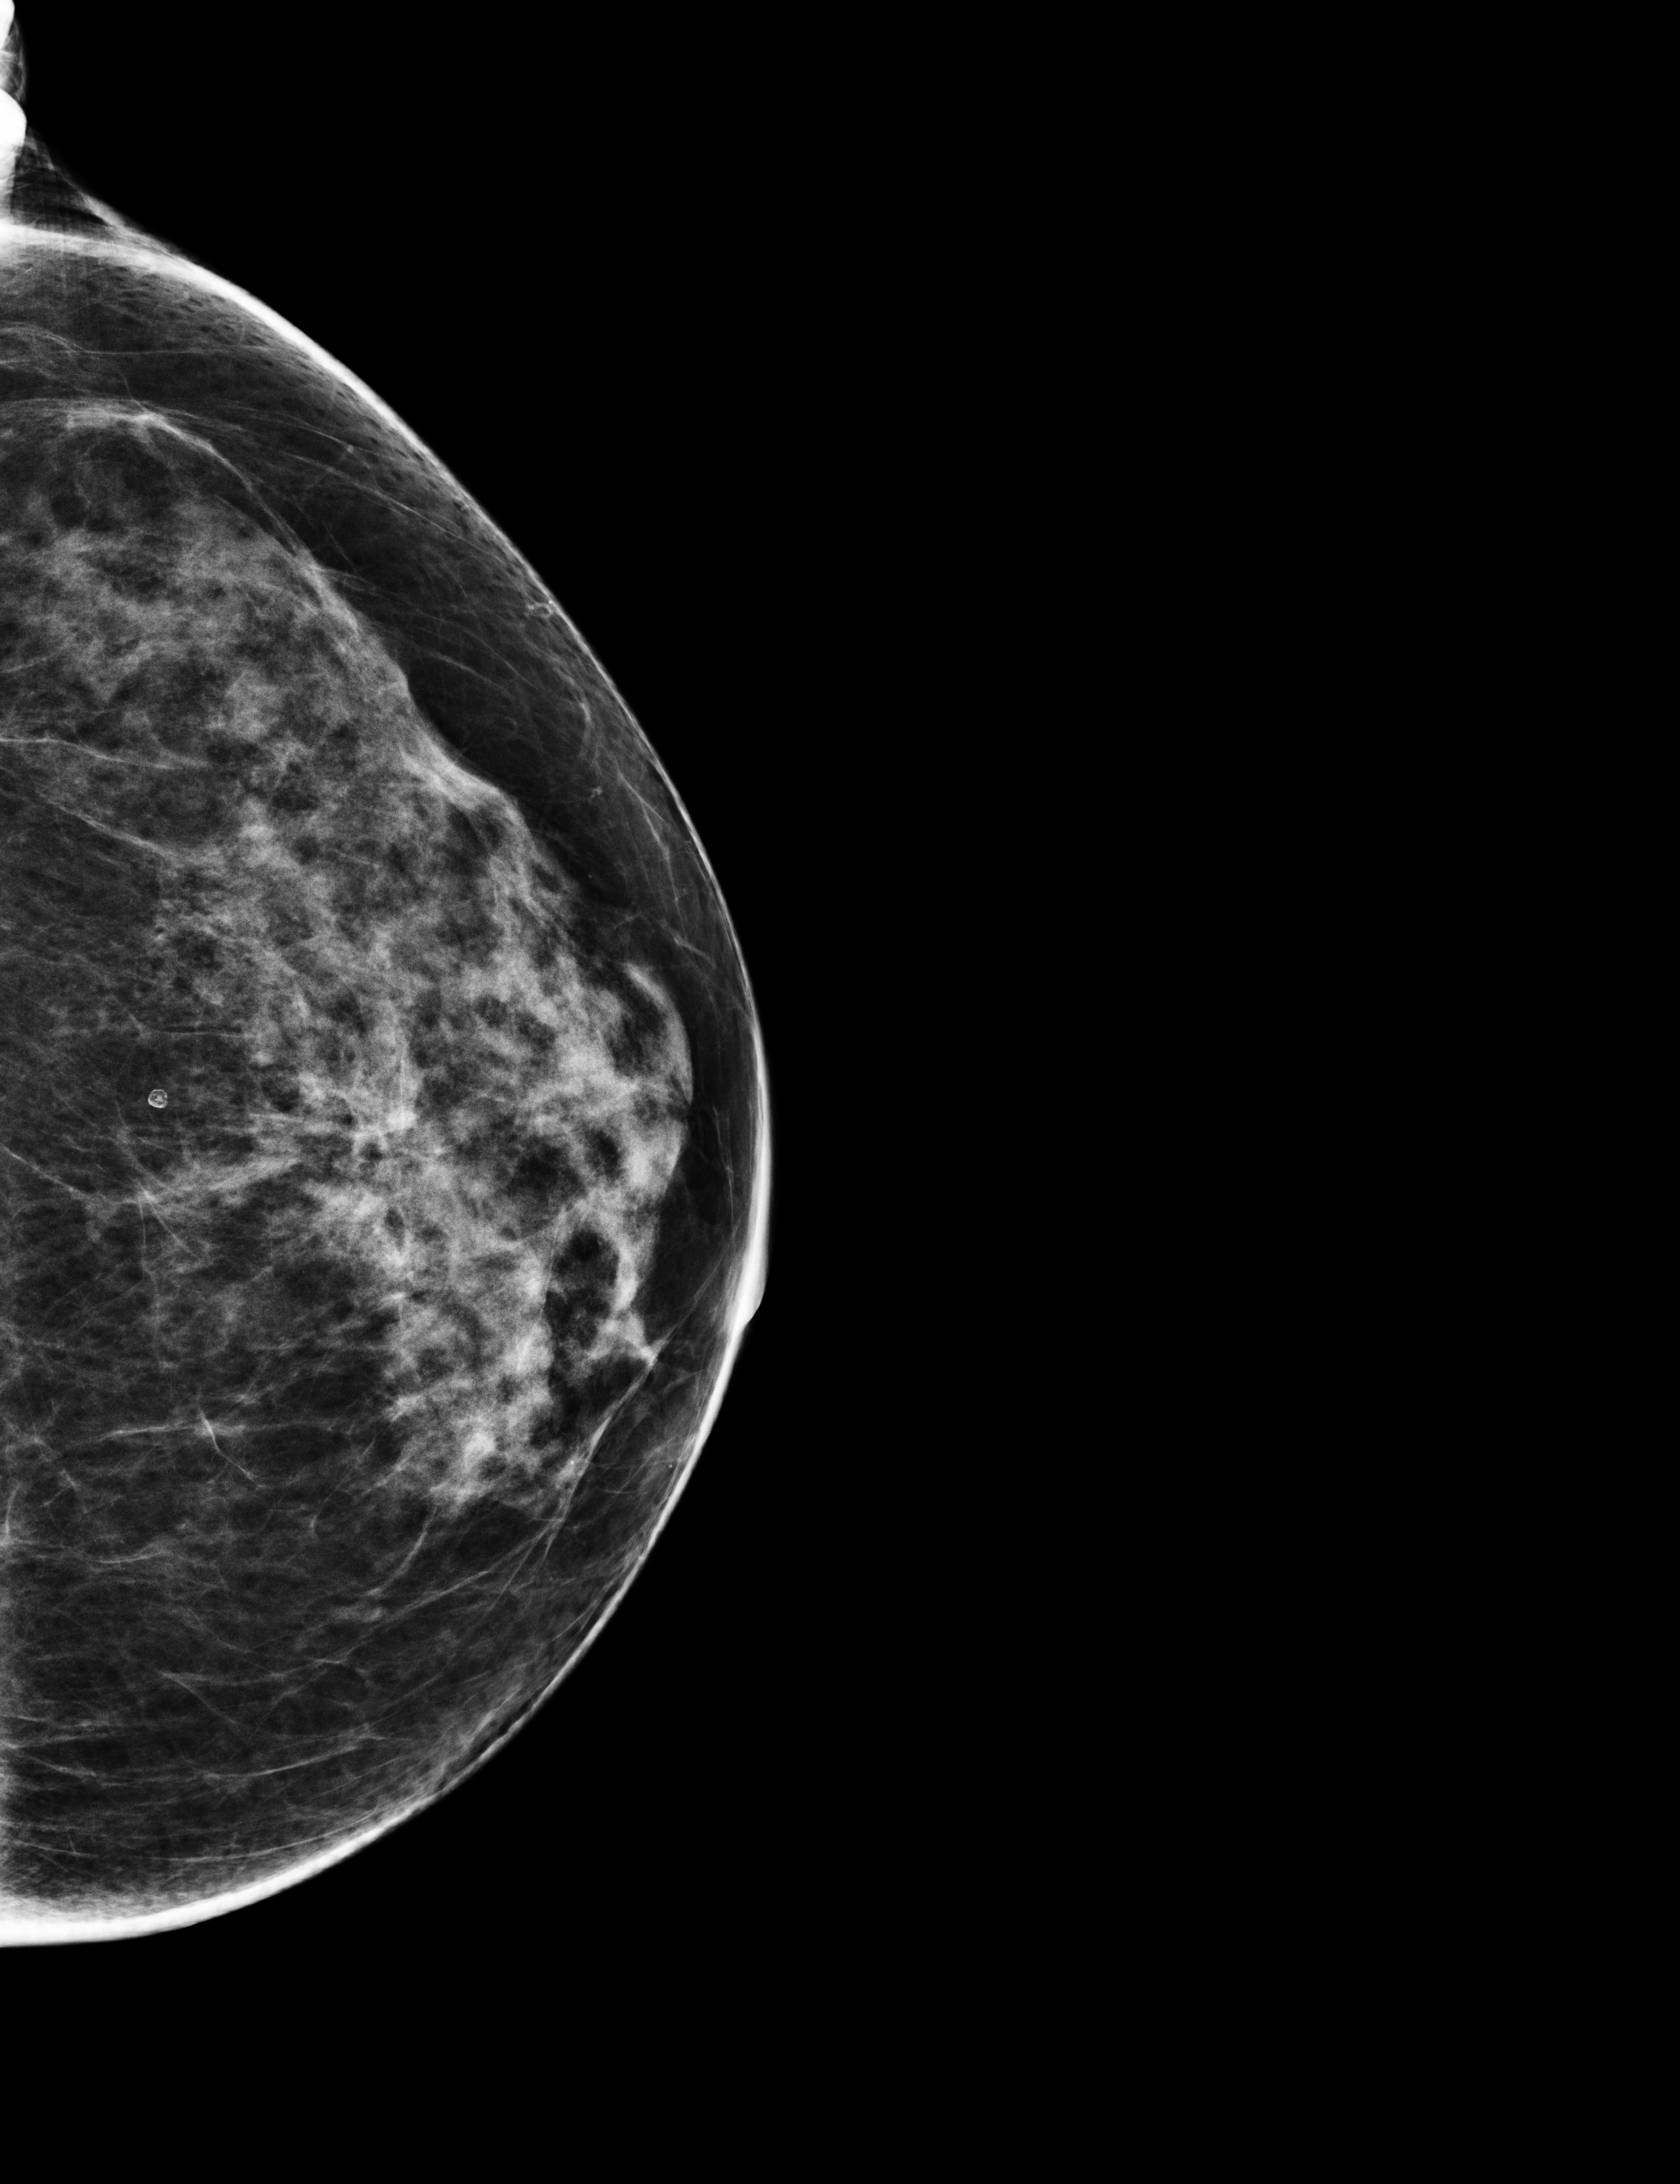
Full-field digital mammogram (FFDM), left breast, CC view, annual screening mammography examination. Patient: female, 66 years.
Breast density at the screening exam (both breasts): heterogeneously dense (BI-RADS density category c). Final BI-RADS assessment for this screening round (tomosynthesis exam, both breasts): category 1. Recall: no recall after this screen.